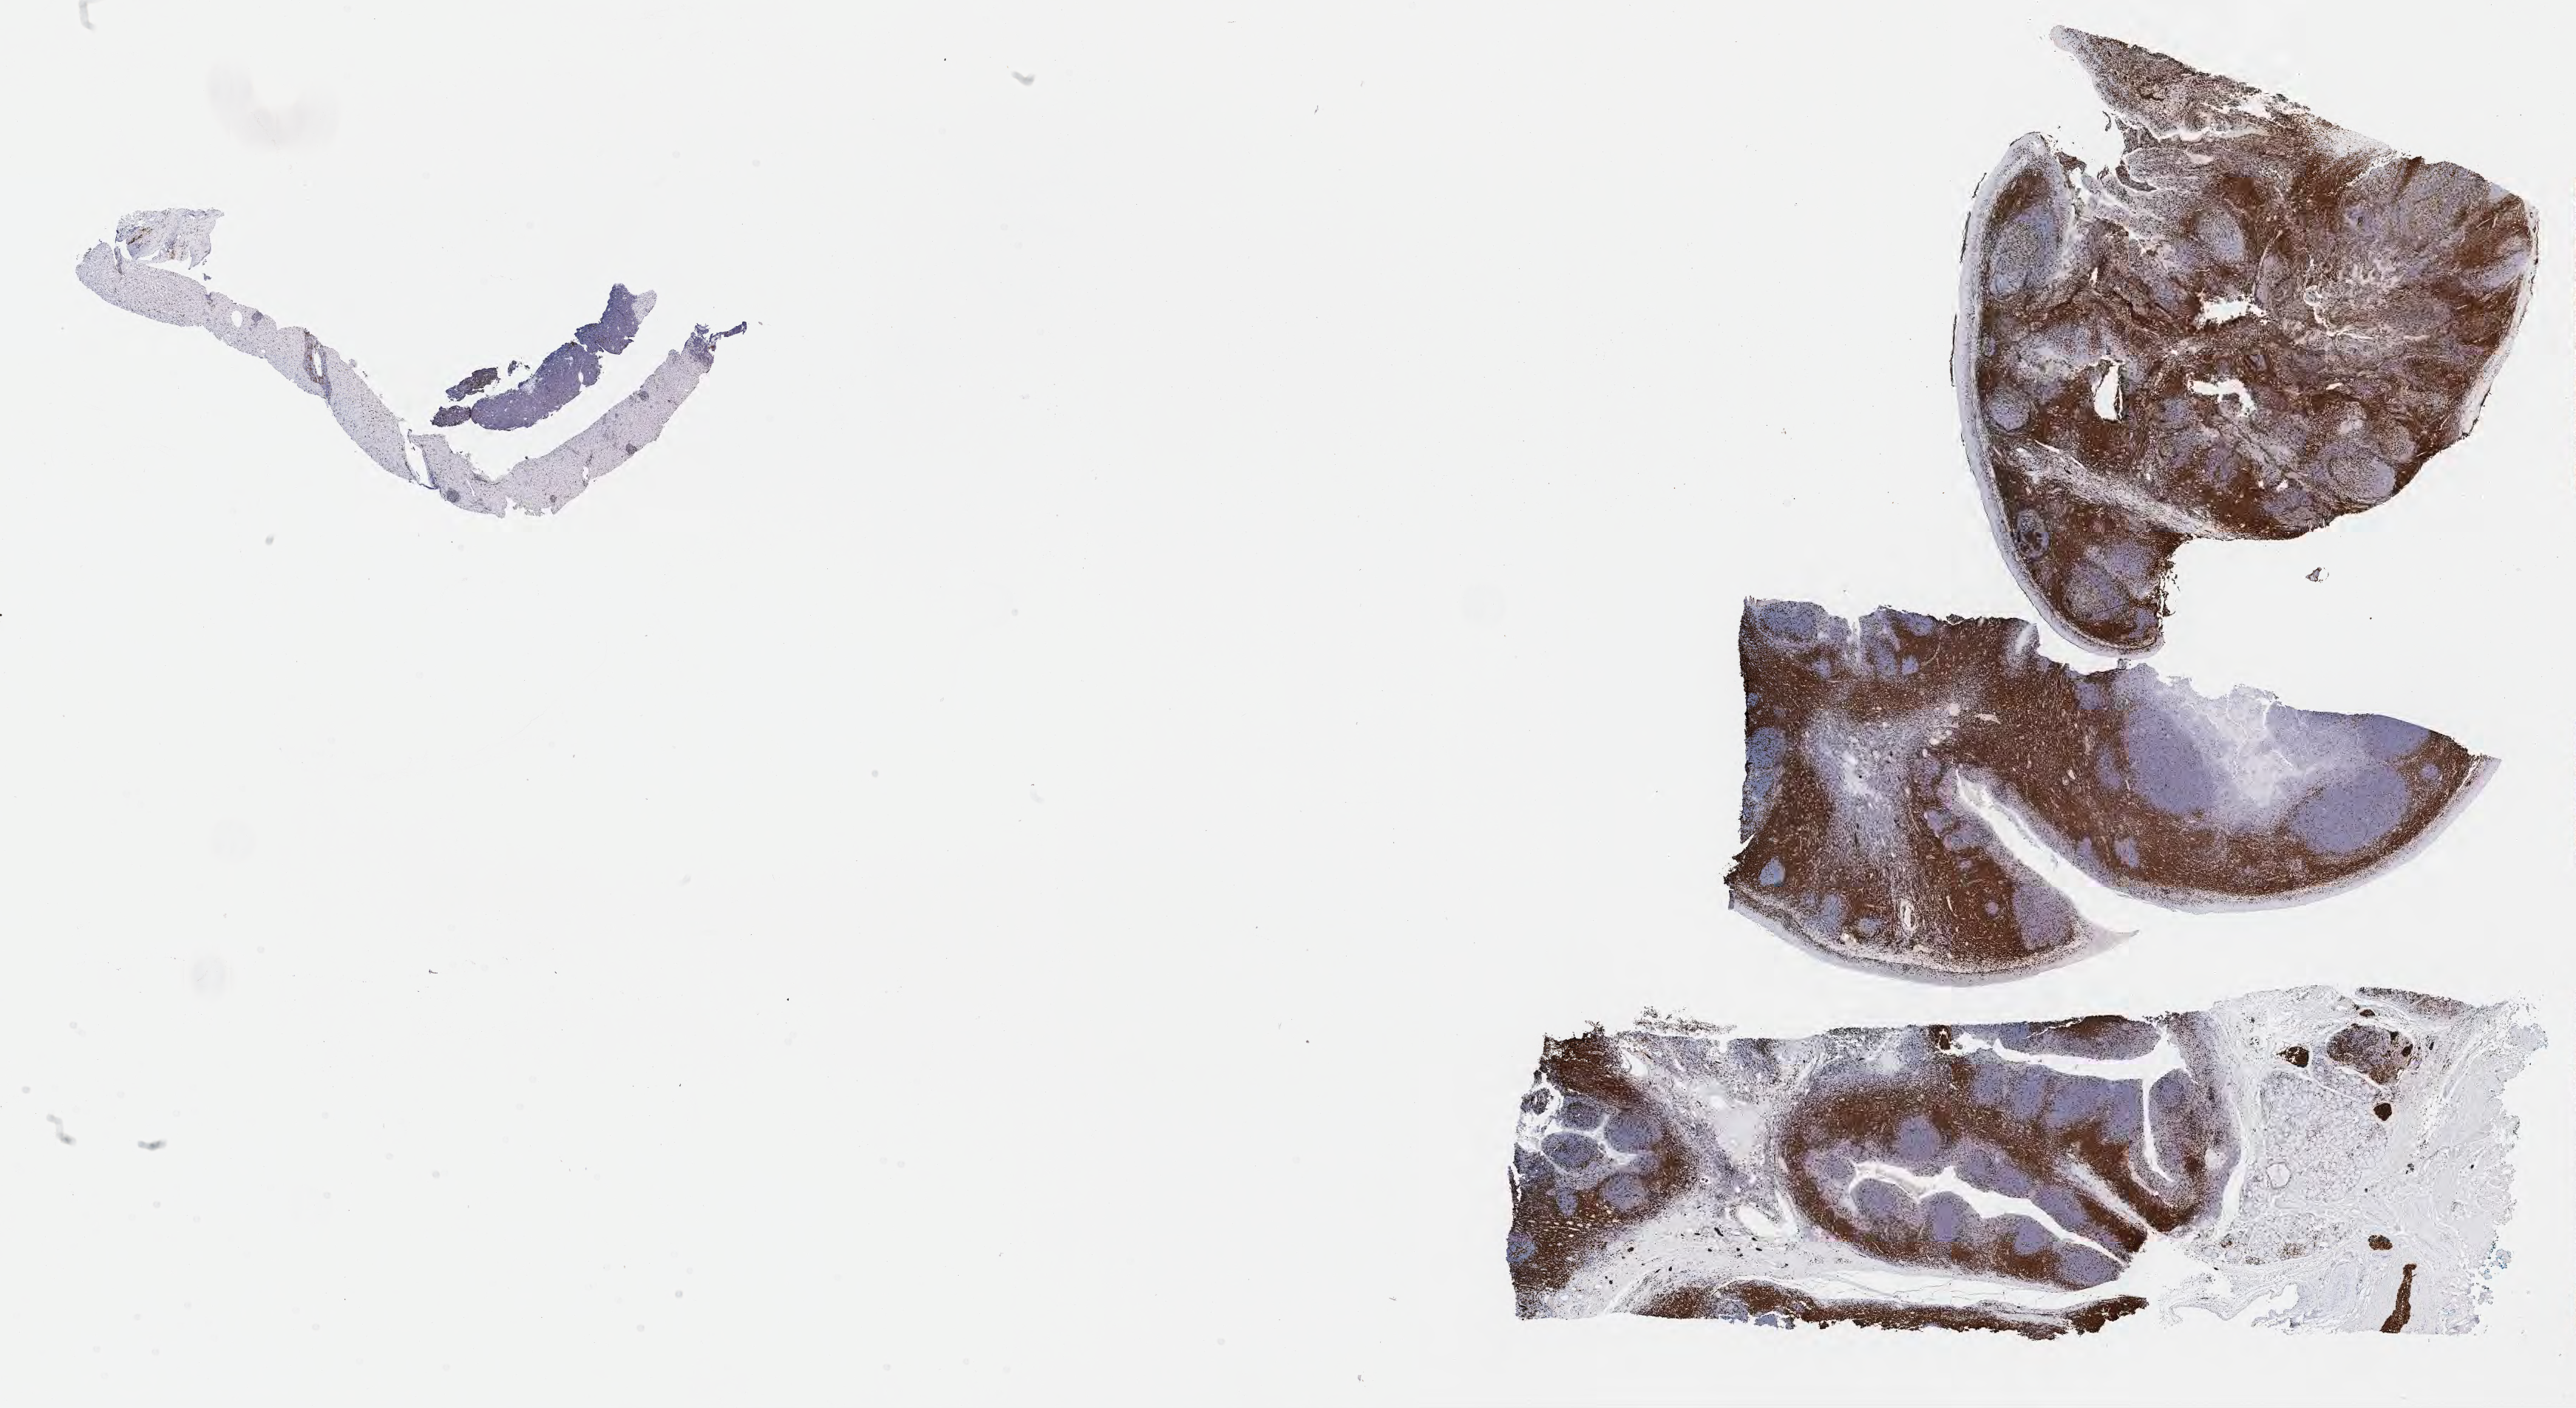
Immunohistochemistry (IHC) whole-slide image stained for CD3, low-resolution overview of the scanned area, about 28.2 x 15.4 mm. Specimen: tumor tissue. Site: liver. Male, age 7 years at initial diagnosis.
Diagnosis: Burkitt lymphoma, NOS.